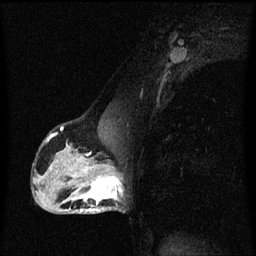
Breast MRI (dynamic contrast-enhanced), one sagittal slice; slice 36 of 60 in the series (ordered by position); dynamic contrast-enhanced series, image 2 of 3 at this slice position (ordered by acquisition); 1.5 T; TE 4.2 ms, TR 8.4 ms; 256 × 256 image matrix. Patient: female, 40 years.
Outlined on this slice (semi-automatic segmentation, software-assisted and operator-edited):
- analysis volume of interest (the breast-tissue region the enhancement analysis was run in; not a lesion): box from (x=76, y=172) to (x=124, y=213) px
- tumour enhancement mask (voxels above the 70 % enhancement threshold inside the analysis volume of interest): (x=76, y=172)–(x=124, y=213)